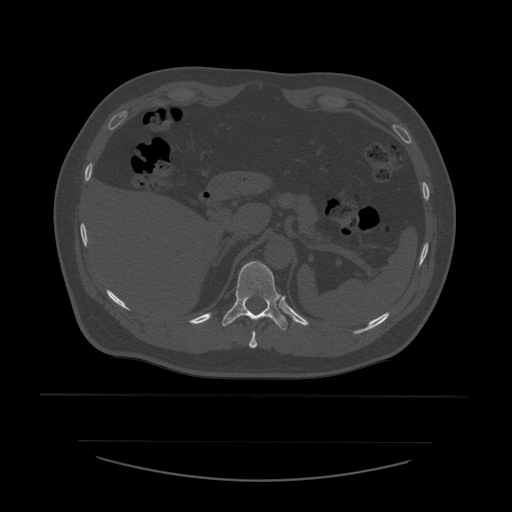
CT including the spine, one axial slice. 120 kVp. Bone window (W 1800 / L 400 HU). 512 × 512 image matrix, field of view 441 × 441 mm. Patient age 44 years. From the clinical record (not read from this slice): primary cancer: soft tissue sarcoma.
Structures marked on this image (semi-automatically segmented with operator editing):
- T10 vertebra: bounding box [x1, y1, x2, y2] px = [249, 331, 258, 349]
- T11 vertebra: [222, 262, 288, 331]